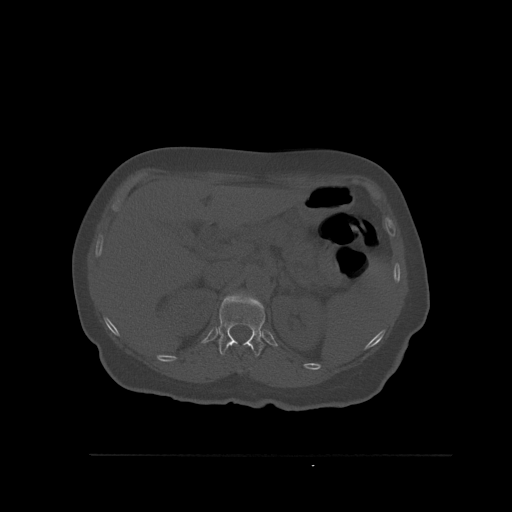
CT including the spine, one axial slice. Position 286 of 527 along the scan axis. Bone window (W 1800 / L 400 HU). 1.5 mm slice thickness. 512 × 512 image matrix. Patient: female, 73 years. From the clinical record (not read from this slice): primary cancer: breast; vertebrae with lytic lesions (as recorded): L2.
Outlined on this slice (semi-automatically segmented with operator editing):
- T11 vertebra: bounding box (x1, y1, x2, y2) in pixels: (239, 370, 241, 372)
- T12 vertebra: (218, 293, 265, 357)